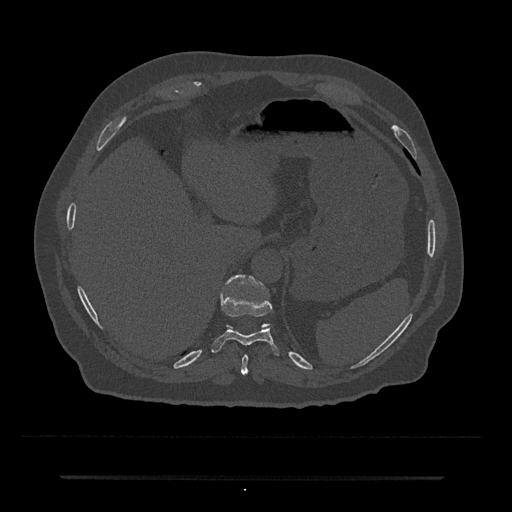
CT including the spine, one axial slice; slice 226 of 797 in the series (ordered by position); bone window (W 1800 / L 400 HU); 0.5 mm slice thickness; 512 × 512 image matrix. Patient: male, 69 years. Case-level facts recorded for this patient, not image findings: primary cancer: prostate.
Annotated regions visible in this slice (semi-automatic segmentation, software-assisted and operator-edited):
- T10 vertebra: bounding box (x1, y1, x2, y2) in pixels: (211, 276, 279, 356)
- T11 vertebra: (224, 275, 269, 327)
- T9 vertebra: (241, 354, 248, 375)